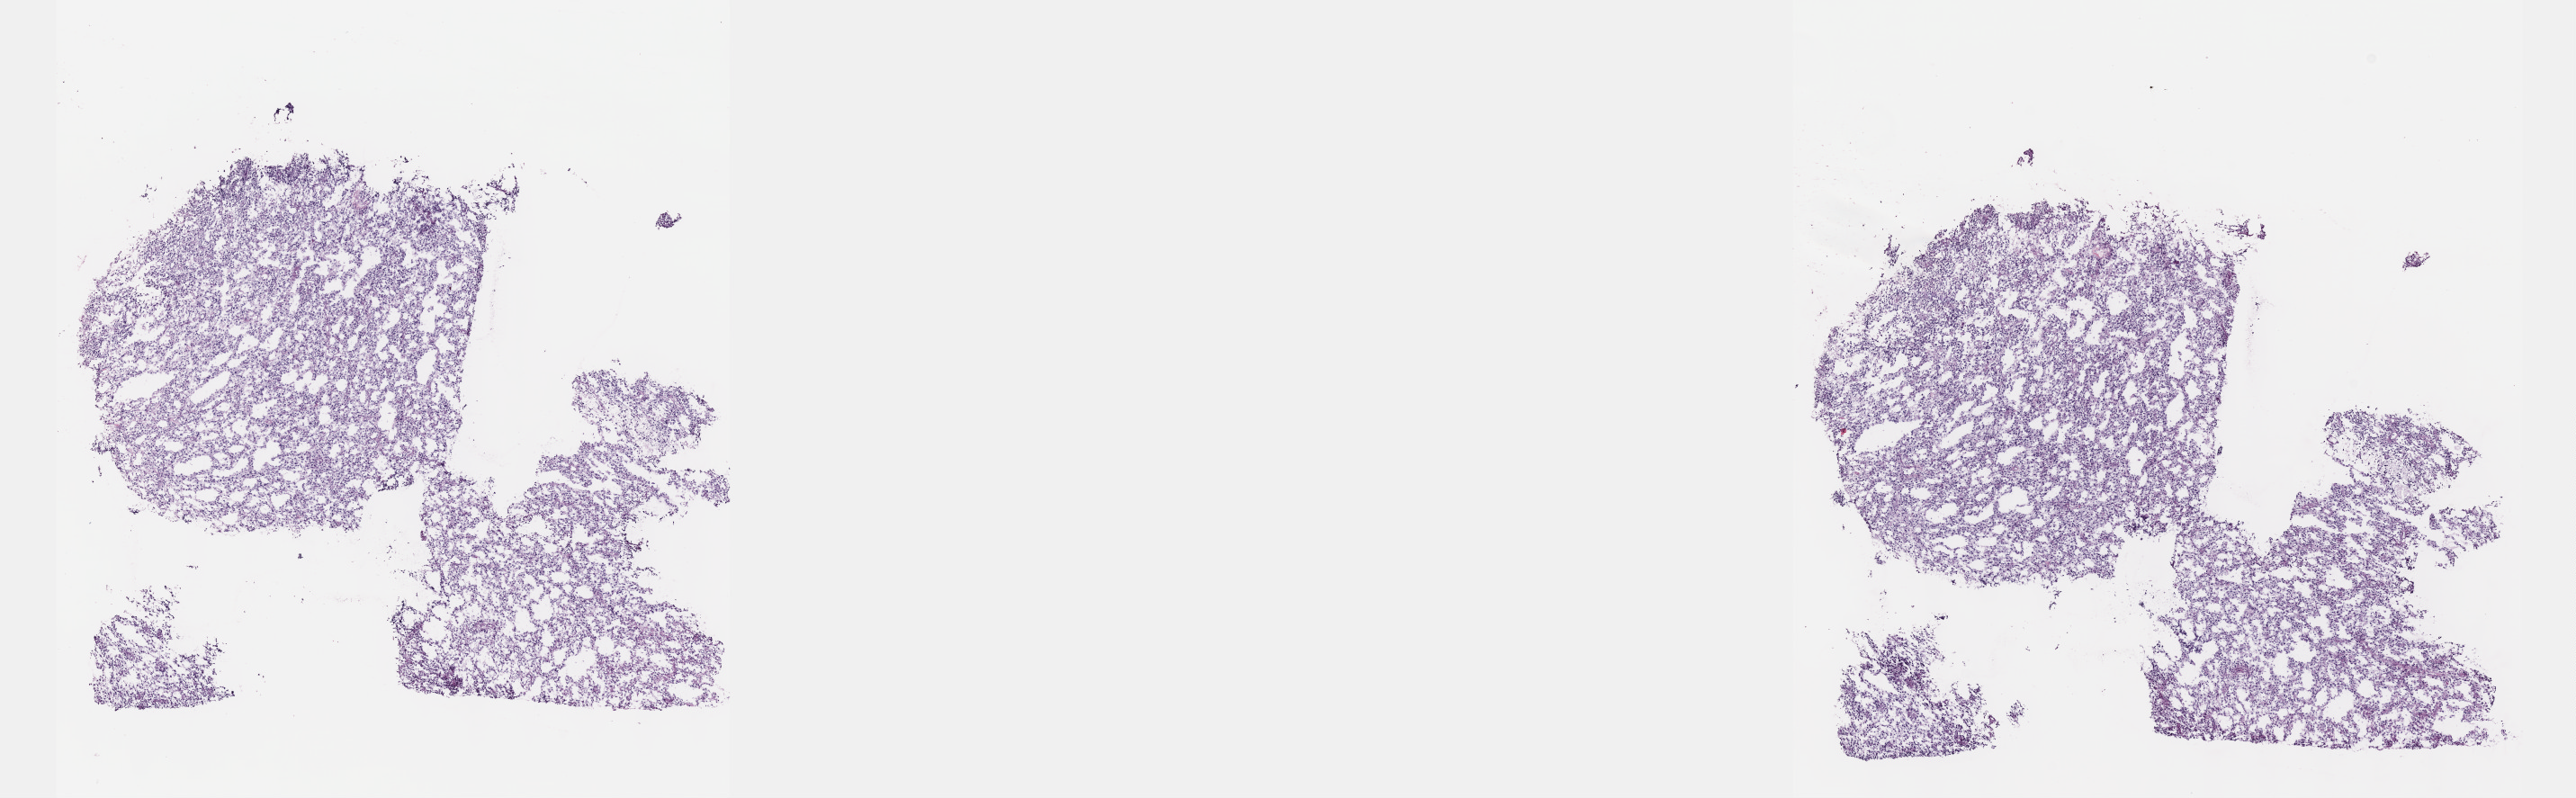
Digitized Hematoxylin and eosin (H&E) stained tissue section (whole slide) — shown as a low-resolution overview of the whole scanned area (about 23.1 x 7.2 mm, from a 40x scan). Frozen section from the top of the tissue portion. Brain, primary tumour sample. Patient: male, age at initial diagnosis 32 years. Histologic grade: G2 (moderately differentiated). Slide review estimates, as recorded: tumour cells 80%, tumour nuclei 95%, normal cells 5%, stromal cells 15%, necrosis 0%. Infiltration values recorded for this section: lymphocyte infiltration 0%, monocyte infiltration 0%, neutrophil infiltration 0%.
Histologic diagnosis: Oligodendroglioma, NOS (cerebrum).